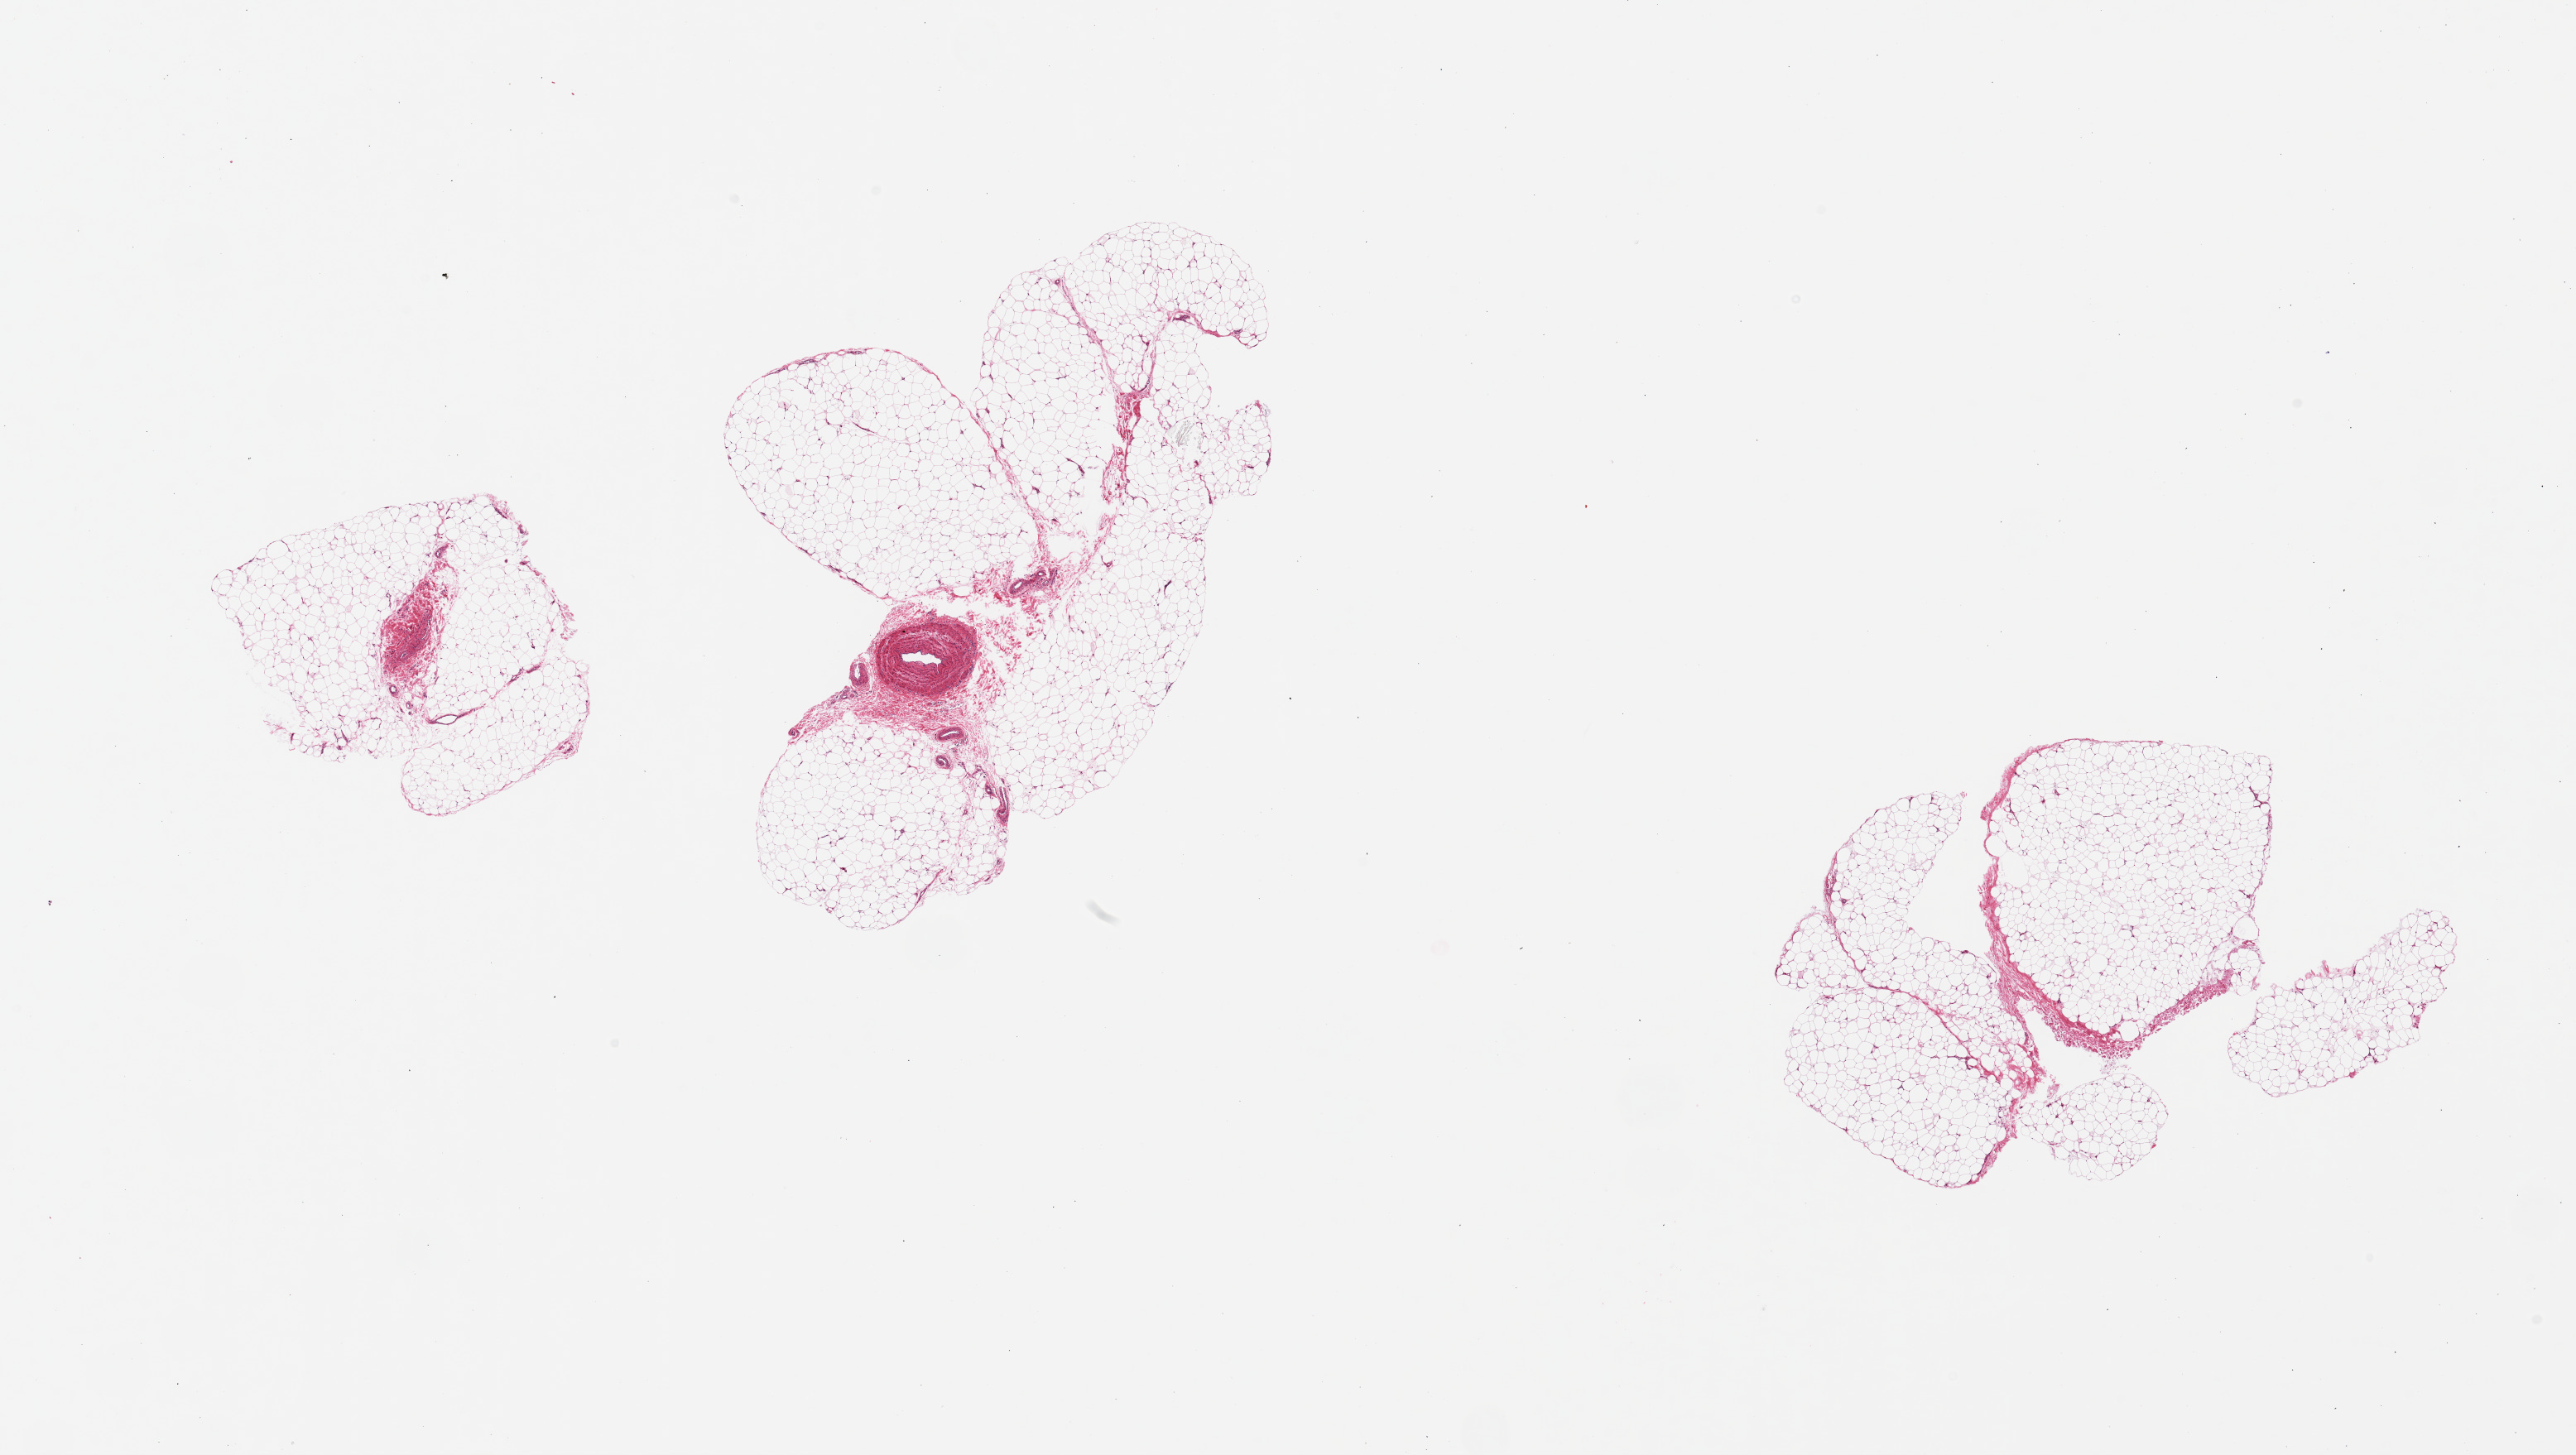
Digitized hematoxylin and eosin (H&E)-stained section, low-resolution overview of the scanned area, about 24.6 x 13.9 mm, PAXgene-fixed, paraffin-embedded tissue, target tissue: adipose tissue, donor tissue sample. Donor sex: female.
Review note (as recorded): 3 pieces, fascia/vascular elements ~10% of tissue.